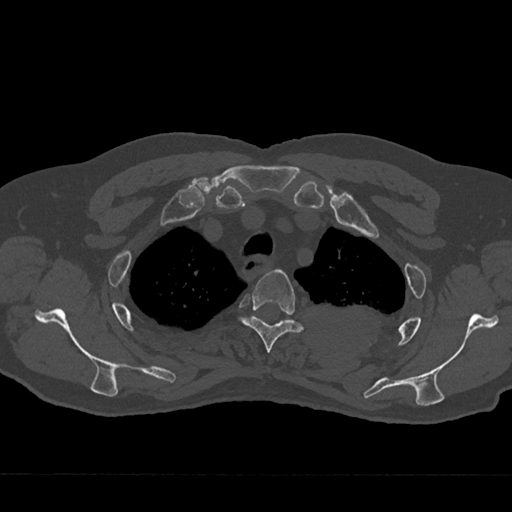
CT including the spine, one axial slice; position 567 of 797 along the scan axis; 120 kVp; bone window (W 1800 / L 400 HU); 0.5 mm slice thickness; 512 × 512 image matrix, field of view 377 × 377 mm. Patient: male, 75 years. Case-level facts recorded for this patient, not image findings: primary cancer: renal; vertebrae with lytic lesions (as recorded): T4.
Annotated regions visible in this slice (semi-automatically segmented with operator editing):
- T3 vertebra: bounding box <239,269,303,353> (left, top, right, bottom; pixels)